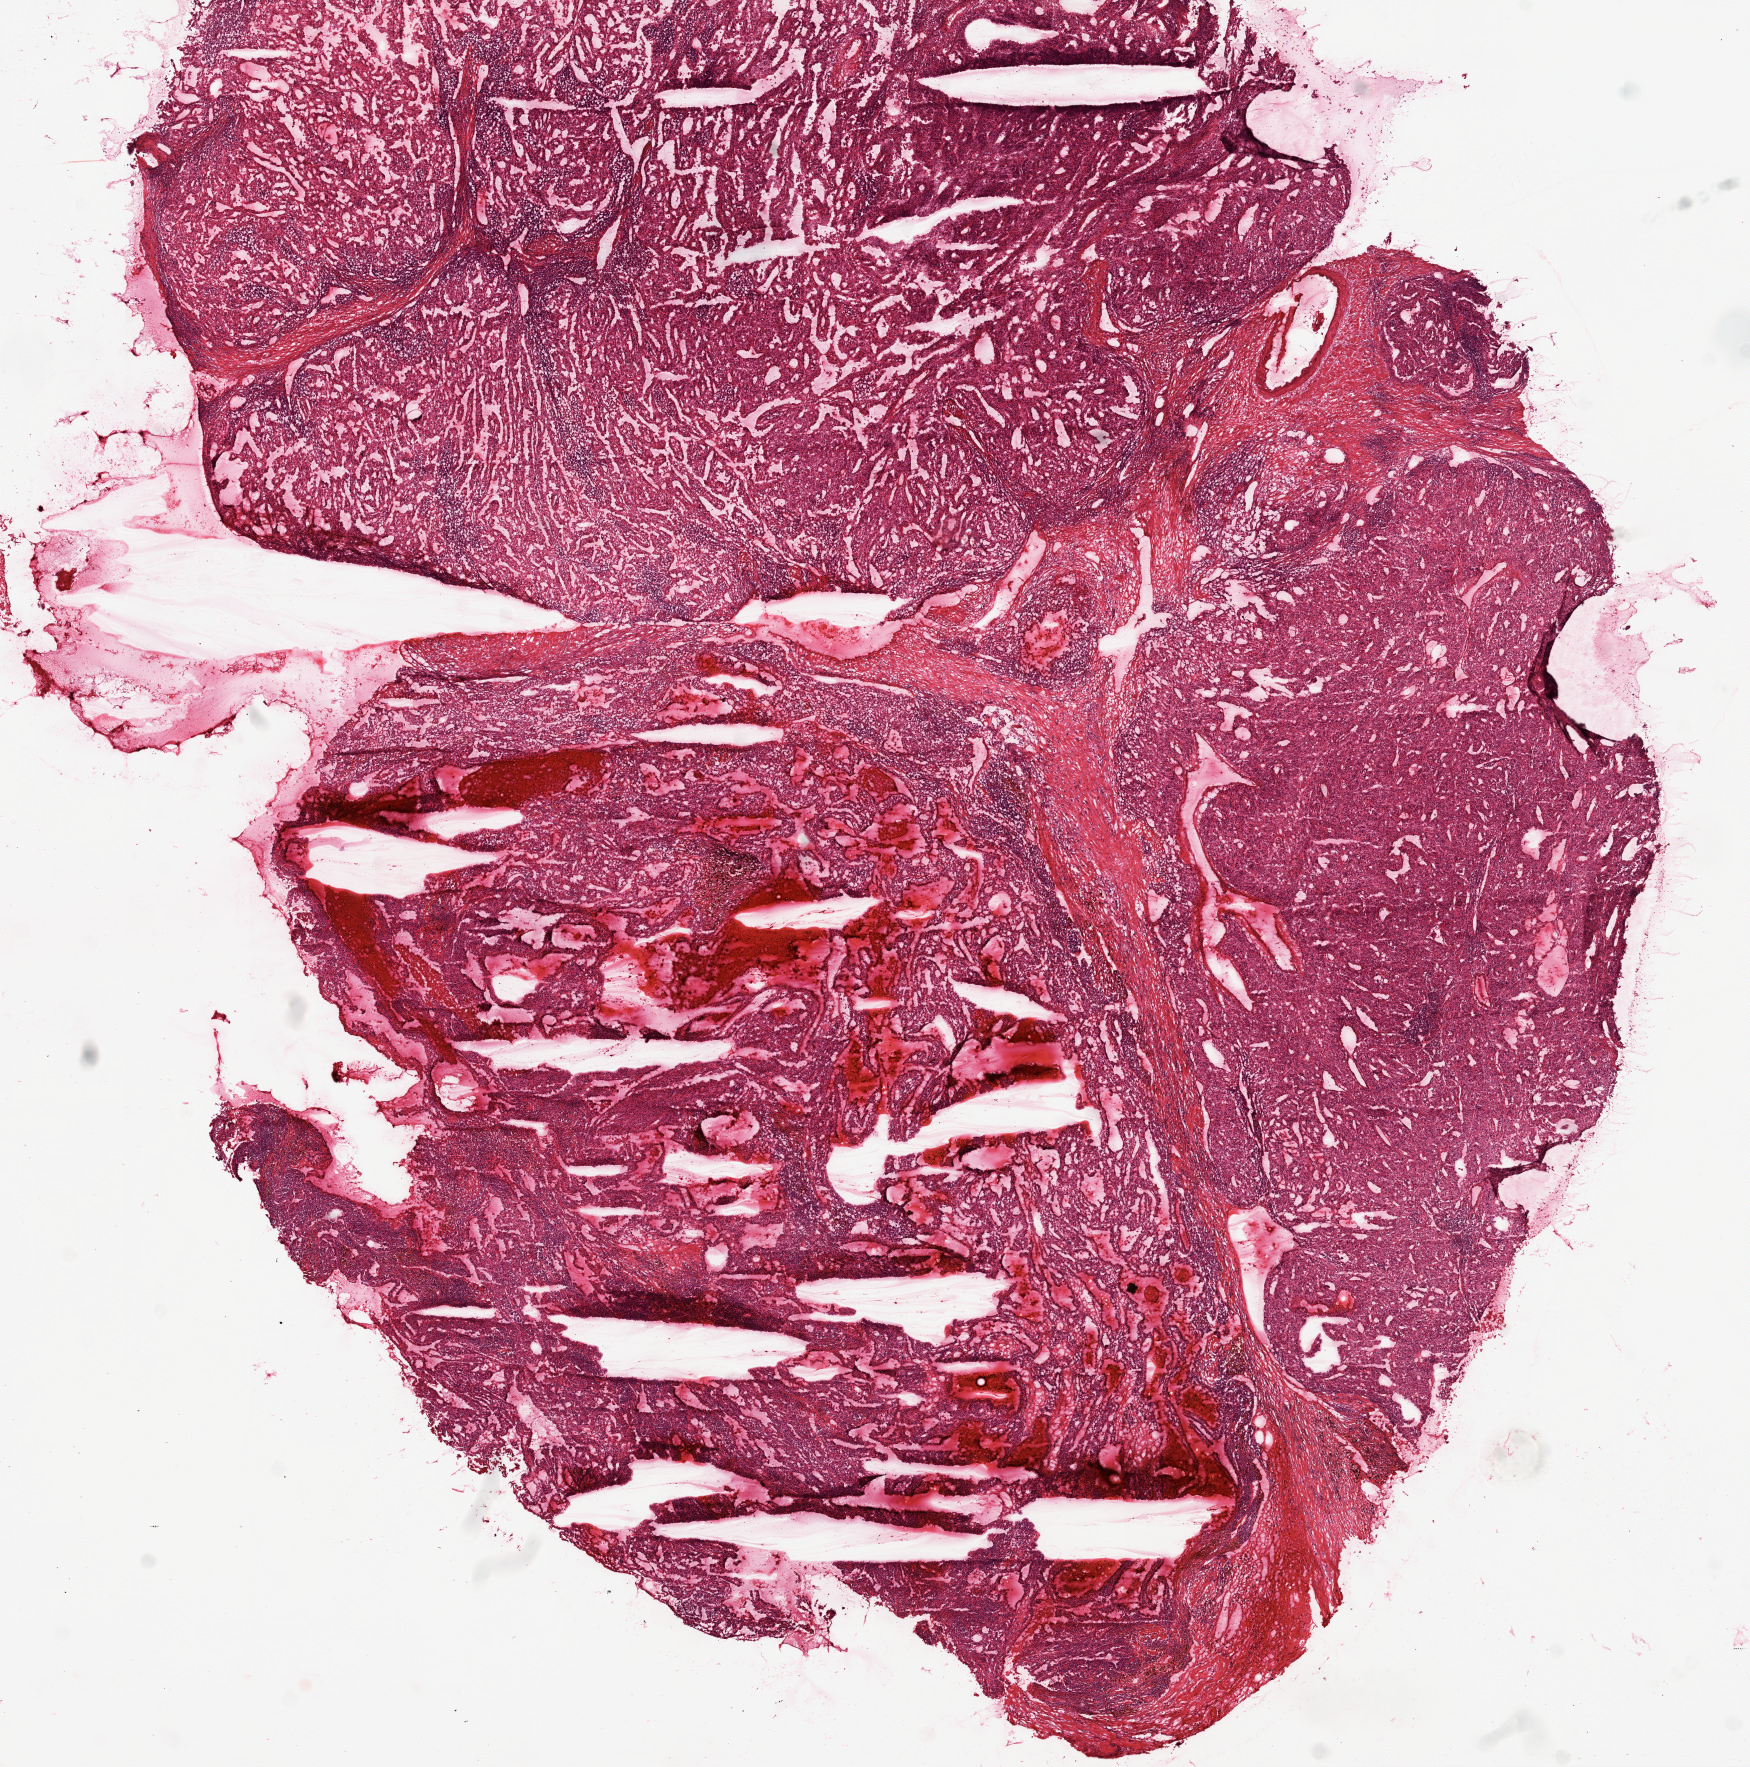
Digitized H&E tissue section (whole slide) — shown as a low-resolution overview of the whole scanned area (about 14.0 x 14.2 mm); frozen section; primary tumour sample from the kidney. Male, age 65 years at initial diagnosis. Histologic grade: G4 (undifferentiated). Composition of this section per pathologist review: tumour cells 85%, tumour nuclei 85%, normal cells 0%, stromal cells 15%, necrosis 0%.
AJCC pathologic stage: III. Pathologic diagnosis: Clear cell adenocarcinoma, NOS.